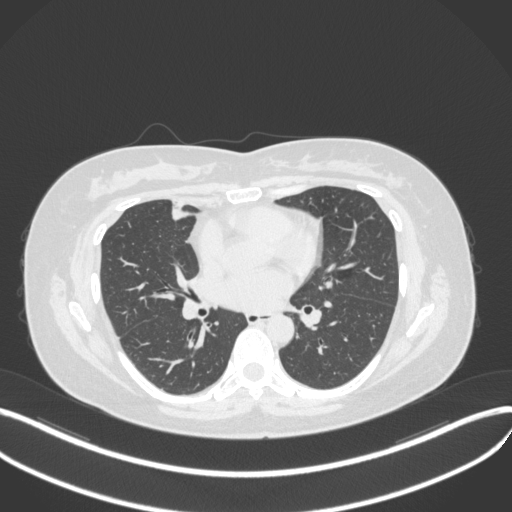
Chest CT, one axial slice; position 155 of 272 along the scan axis; 120 kVp; lung window (W 1500 / L -600 HU); 1 mm slice thickness; 512 × 512 image matrix, field of view 400 × 400 mm. Patient: female, 42 years. From the clinical record (not read from this slice): clinical TNM (as recorded): T1b N0 M0.
Structures marked on this image (rectangle marked by the reading radiologist):
- lung tumour (recorded histology: adenocarcinoma): bounding box (x1, y1, x2, y2) in pixels: (165, 194, 198, 223)